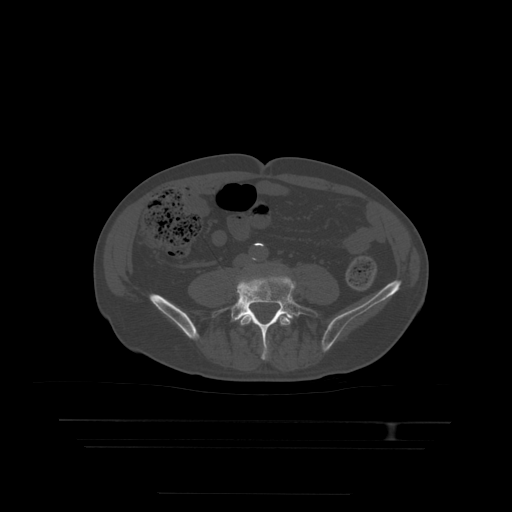
CT including the spine, one axial slice. Slice 80 of 522 in the series (ordered by position). Bone window (W 1800 / L 400 HU). 1.25 mm slice thickness. 512 × 512 image matrix. Patient age 68 years. From the clinical record (not read from this slice): primary cancer: urothelial.
Structures marked on this image (semi-automatically segmented with operator editing):
- L4 vertebra: bounding box [x1, y1, x2, y2] px = [240, 314, 291, 326]
- L5 vertebra: [212, 277, 318, 360]